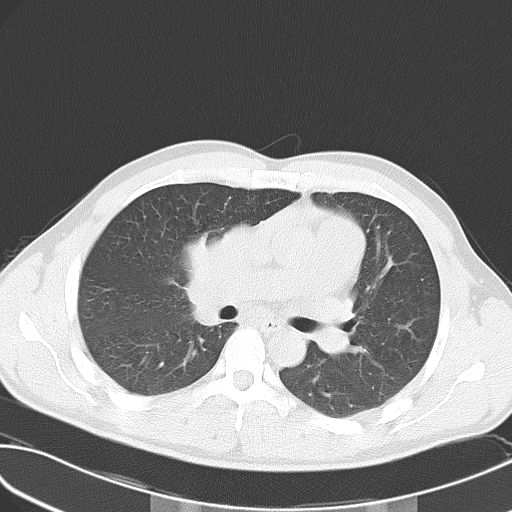
Chest CT, one axial slice; slice 32 of 55 in the series (ordered by position); reconstruction kernel B70f; 120 kVp; lung window (W 1500 / L -600 HU); 5 mm slice thickness; 512 × 512 image matrix, field of view 346 × 346 mm. Male patient, age 32 years. Case-level facts recorded for this patient, not image findings: clinical TNM (as recorded): T4 N3 M0.
Annotated regions visible in this slice (bounding box drawn by a radiologist):
- lung tumour (recorded histology: small cell carcinoma): bounding box (x1, y1, x2, y2) in pixels: (173, 221, 247, 328)